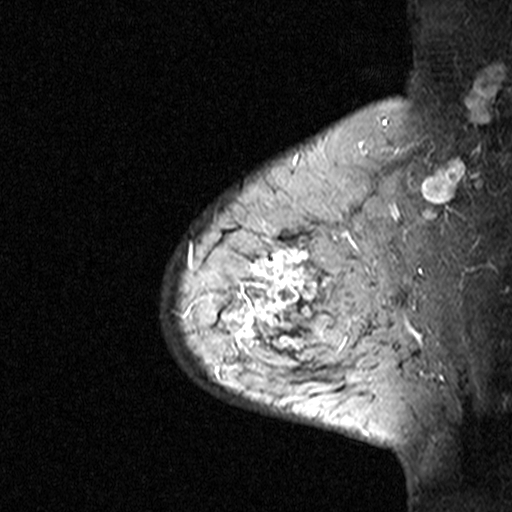
Breast MRI (dynamic contrast-enhanced), one sagittal slice; slice 33 of 44 in the series (ordered by position); dynamic contrast-enhanced study with each time point stored as its own series, time point 3 of 4 at this slice position (ordered by acquisition time); 1.5 T; TE 4.5 ms, TR 11 ms; 512 × 512 image matrix, field of view 200 × 200 mm. Patient: female, 65 years. Case-level facts recorded for this patient, not image findings: setting: breast cancer imaged before/during neoadjuvant chemotherapy; receptor status: HER2-positive.
Structures marked on this image (semi-automatically segmented with operator editing):
- analysis volume of interest (the breast-tissue region the enhancement analysis was run in; not a lesion): box from (x=182, y=190) to (x=353, y=361) px
- tumour enhancement mask (voxels above the 90 % enhancement threshold inside the analysis volume of interest): (x=189, y=240)–(x=328, y=350)